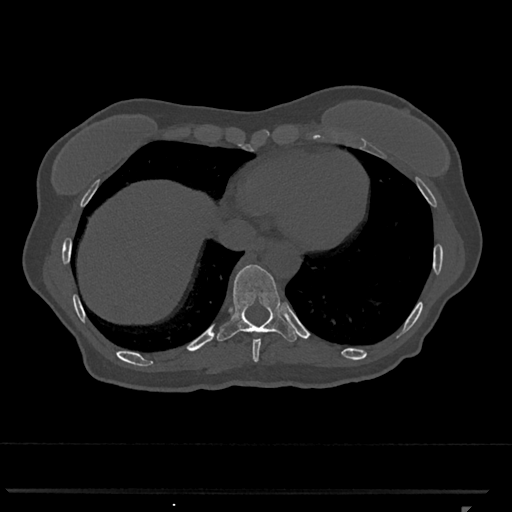
CT including the spine, one axial slice; position 580 of 793 along the scan axis; reconstruction kernel Br40s/3; bone window (W 1800 / L 400 HU); 0.5 mm slice thickness; 512 × 512 image matrix. Patient: female, 62 years. From the clinical record (not read from this slice): primary cancer: renal.
Annotated regions visible in this slice (semi-automatically segmented with operator editing):
- T10 vertebra: bounding box (x1, y1, x2, y2) in pixels: (217, 264, 298, 342)
- T9 vertebra: (252, 339, 261, 362)